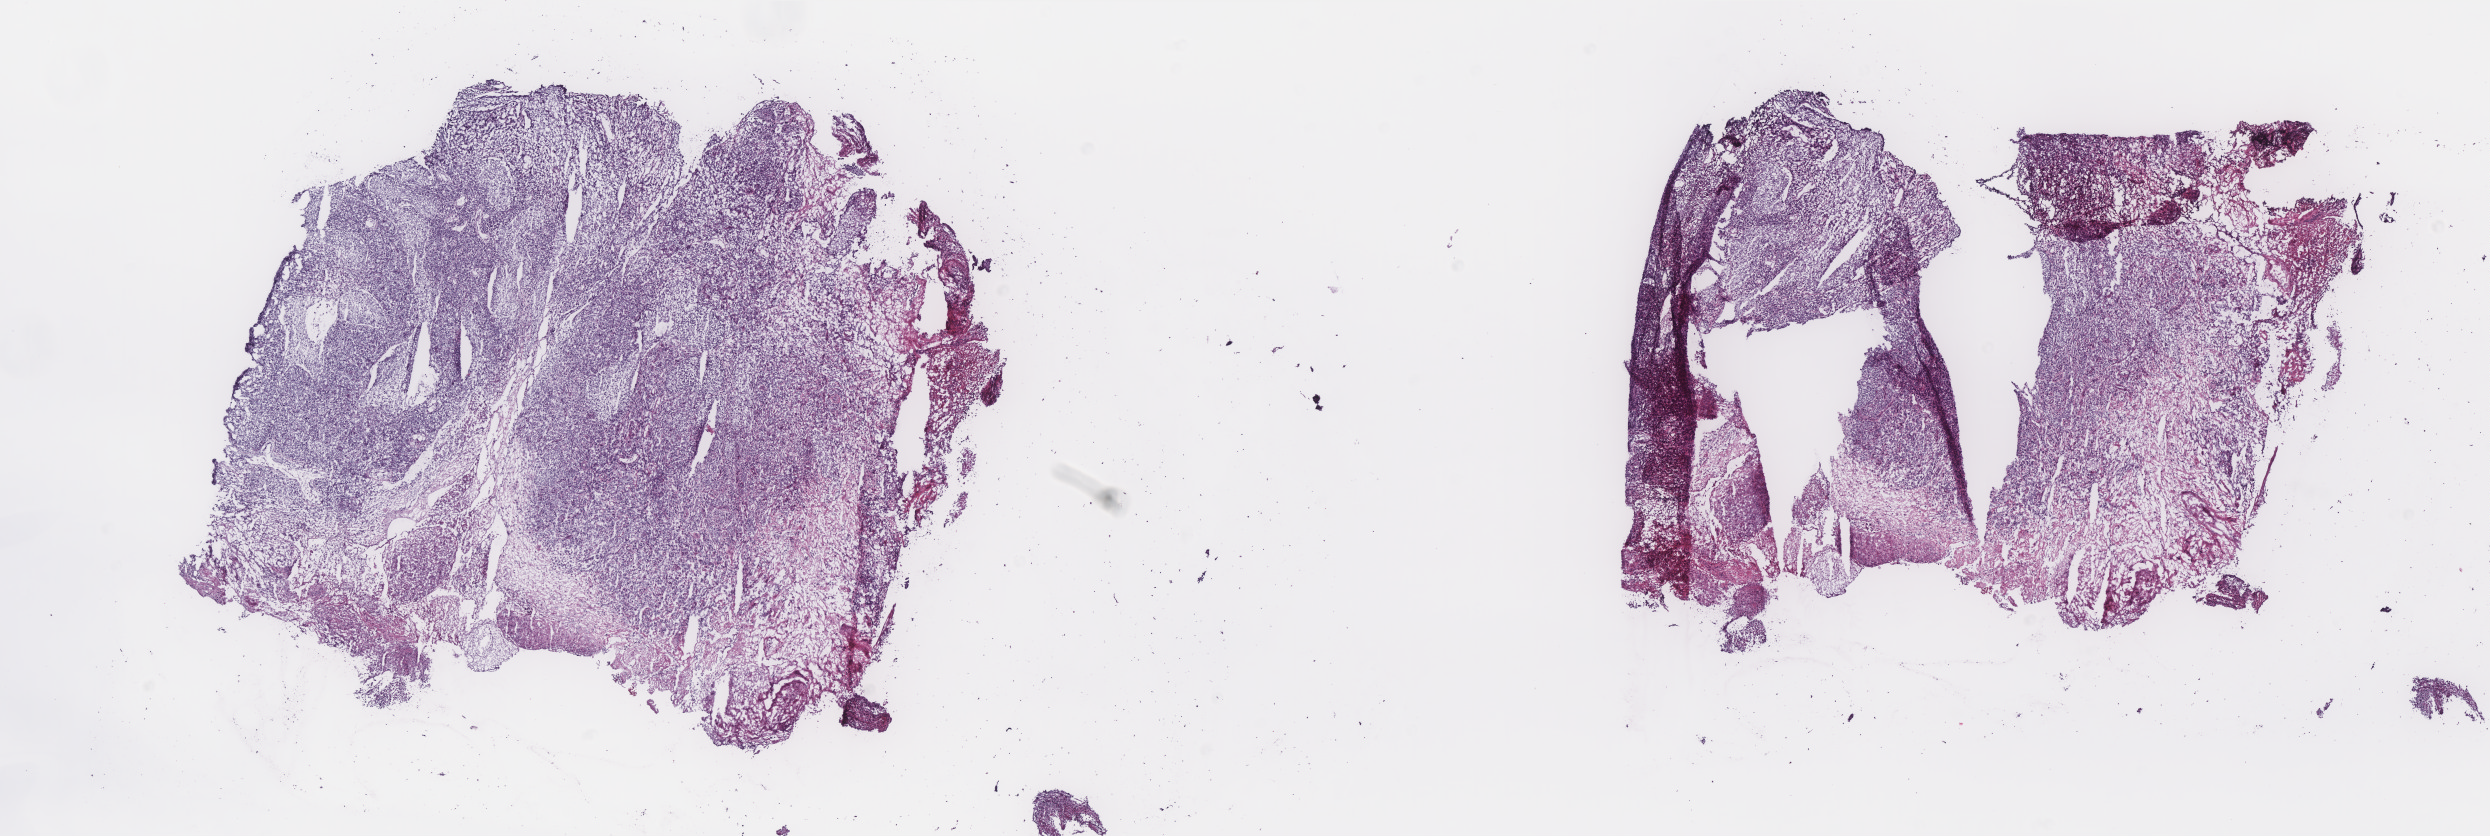
Digitized Hematoxylin and eosin (H&E) stained tissue section (whole slide) — a low-resolution overview of the entire scanned area, about 20.0 x 6.7 mm (slide scanned at 40x). Frozen section from the top of the tissue portion. Sample: primary tumour, cervix. Female patient; age at initial diagnosis 46 years. Histologic grade: G1 (well differentiated). Composition of this section per pathologist review: tumour cells 65%, tumour nuclei 70%, normal cells 0%, stromal cells 30%, necrosis 5%. Inflammatory infiltration, as recorded: lymphocyte infiltration 15%, monocyte infiltration 1%, neutrophil infiltration 3%.
Lymph nodes positive (case pathology): 0 of 33 examined. FIGO stage: IB. Histologic diagnosis: Squamous cell carcinoma, NOS (cervix uteri).